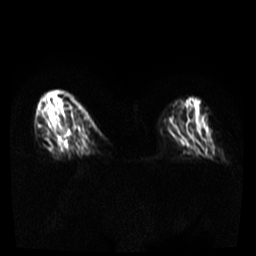
Breast MRI, one axial slice; position 12 of 36 along the scan axis; diffusion-weighted series; image 2 of 4 stored at this slice position (different b-values; order by instance number); 3 T; 5 mm slice thickness; 256 × 256 image matrix. Female patient.
Outlined on this slice (expert manual segmentation):
- tumour on diffusion-weighted imaging: bounding box (x1, y1, x2, y2) in pixels: (51, 126, 66, 152)